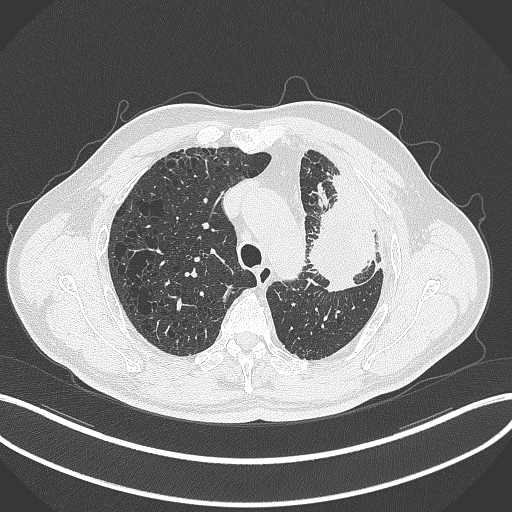
Chest CT, one axial slice. Position 236 of 297 along the scan axis. 120 kVp. Lung window (W 1500 / L -600 HU). 512 × 512 image matrix, field of view 400 × 400 mm. Patient: male, 68 years. From the clinical record (not read from this slice): clinical TNM (as recorded): T3 N3 M1.
Structures marked on this image (bounding box drawn by a radiologist):
- lung tumour (recorded histology: adenocarcinoma): bounding box (x1, y1, x2, y2) in pixels: (305, 166, 392, 299)